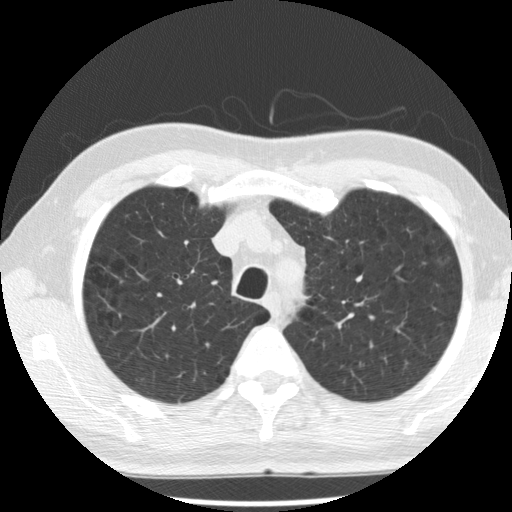
Low-dose screening chest CT, axial slice. Baseline screening round. Lung window (W 1500 / L -600 HU). Slice 58 of 277 in the series. 512 × 512 image matrix. Male, age 68 years at enrolment. Current smoker at enrolment.
Lesion marked by an expert reader, bounding box (x1, y1, x2, y2) in pixels: (431, 248, 466, 281). The exam's reader record, not a measurement of the box and not confirmed to be the same lesion: non-calcified nodule or mass ≥4 mm, left upper lobe, 5 × 5 mm, poorly defined margins, ground glass attenuation. Official screen result: positive, change unspecified: nodule(s) >= 4 mm or enlarging nodule(s), mass(es), or other non-specific abnormalities suspicious for lung cancer. Later outcome: lung cancer diagnosed 648 days after this screen (after the second annual screen) — bronchiolo-alveolar adenocarcinoma, NOS, left upper lobe, moderately differentiated (G2), stage IA (AJCC 6th edition), 17 mm at pathology.